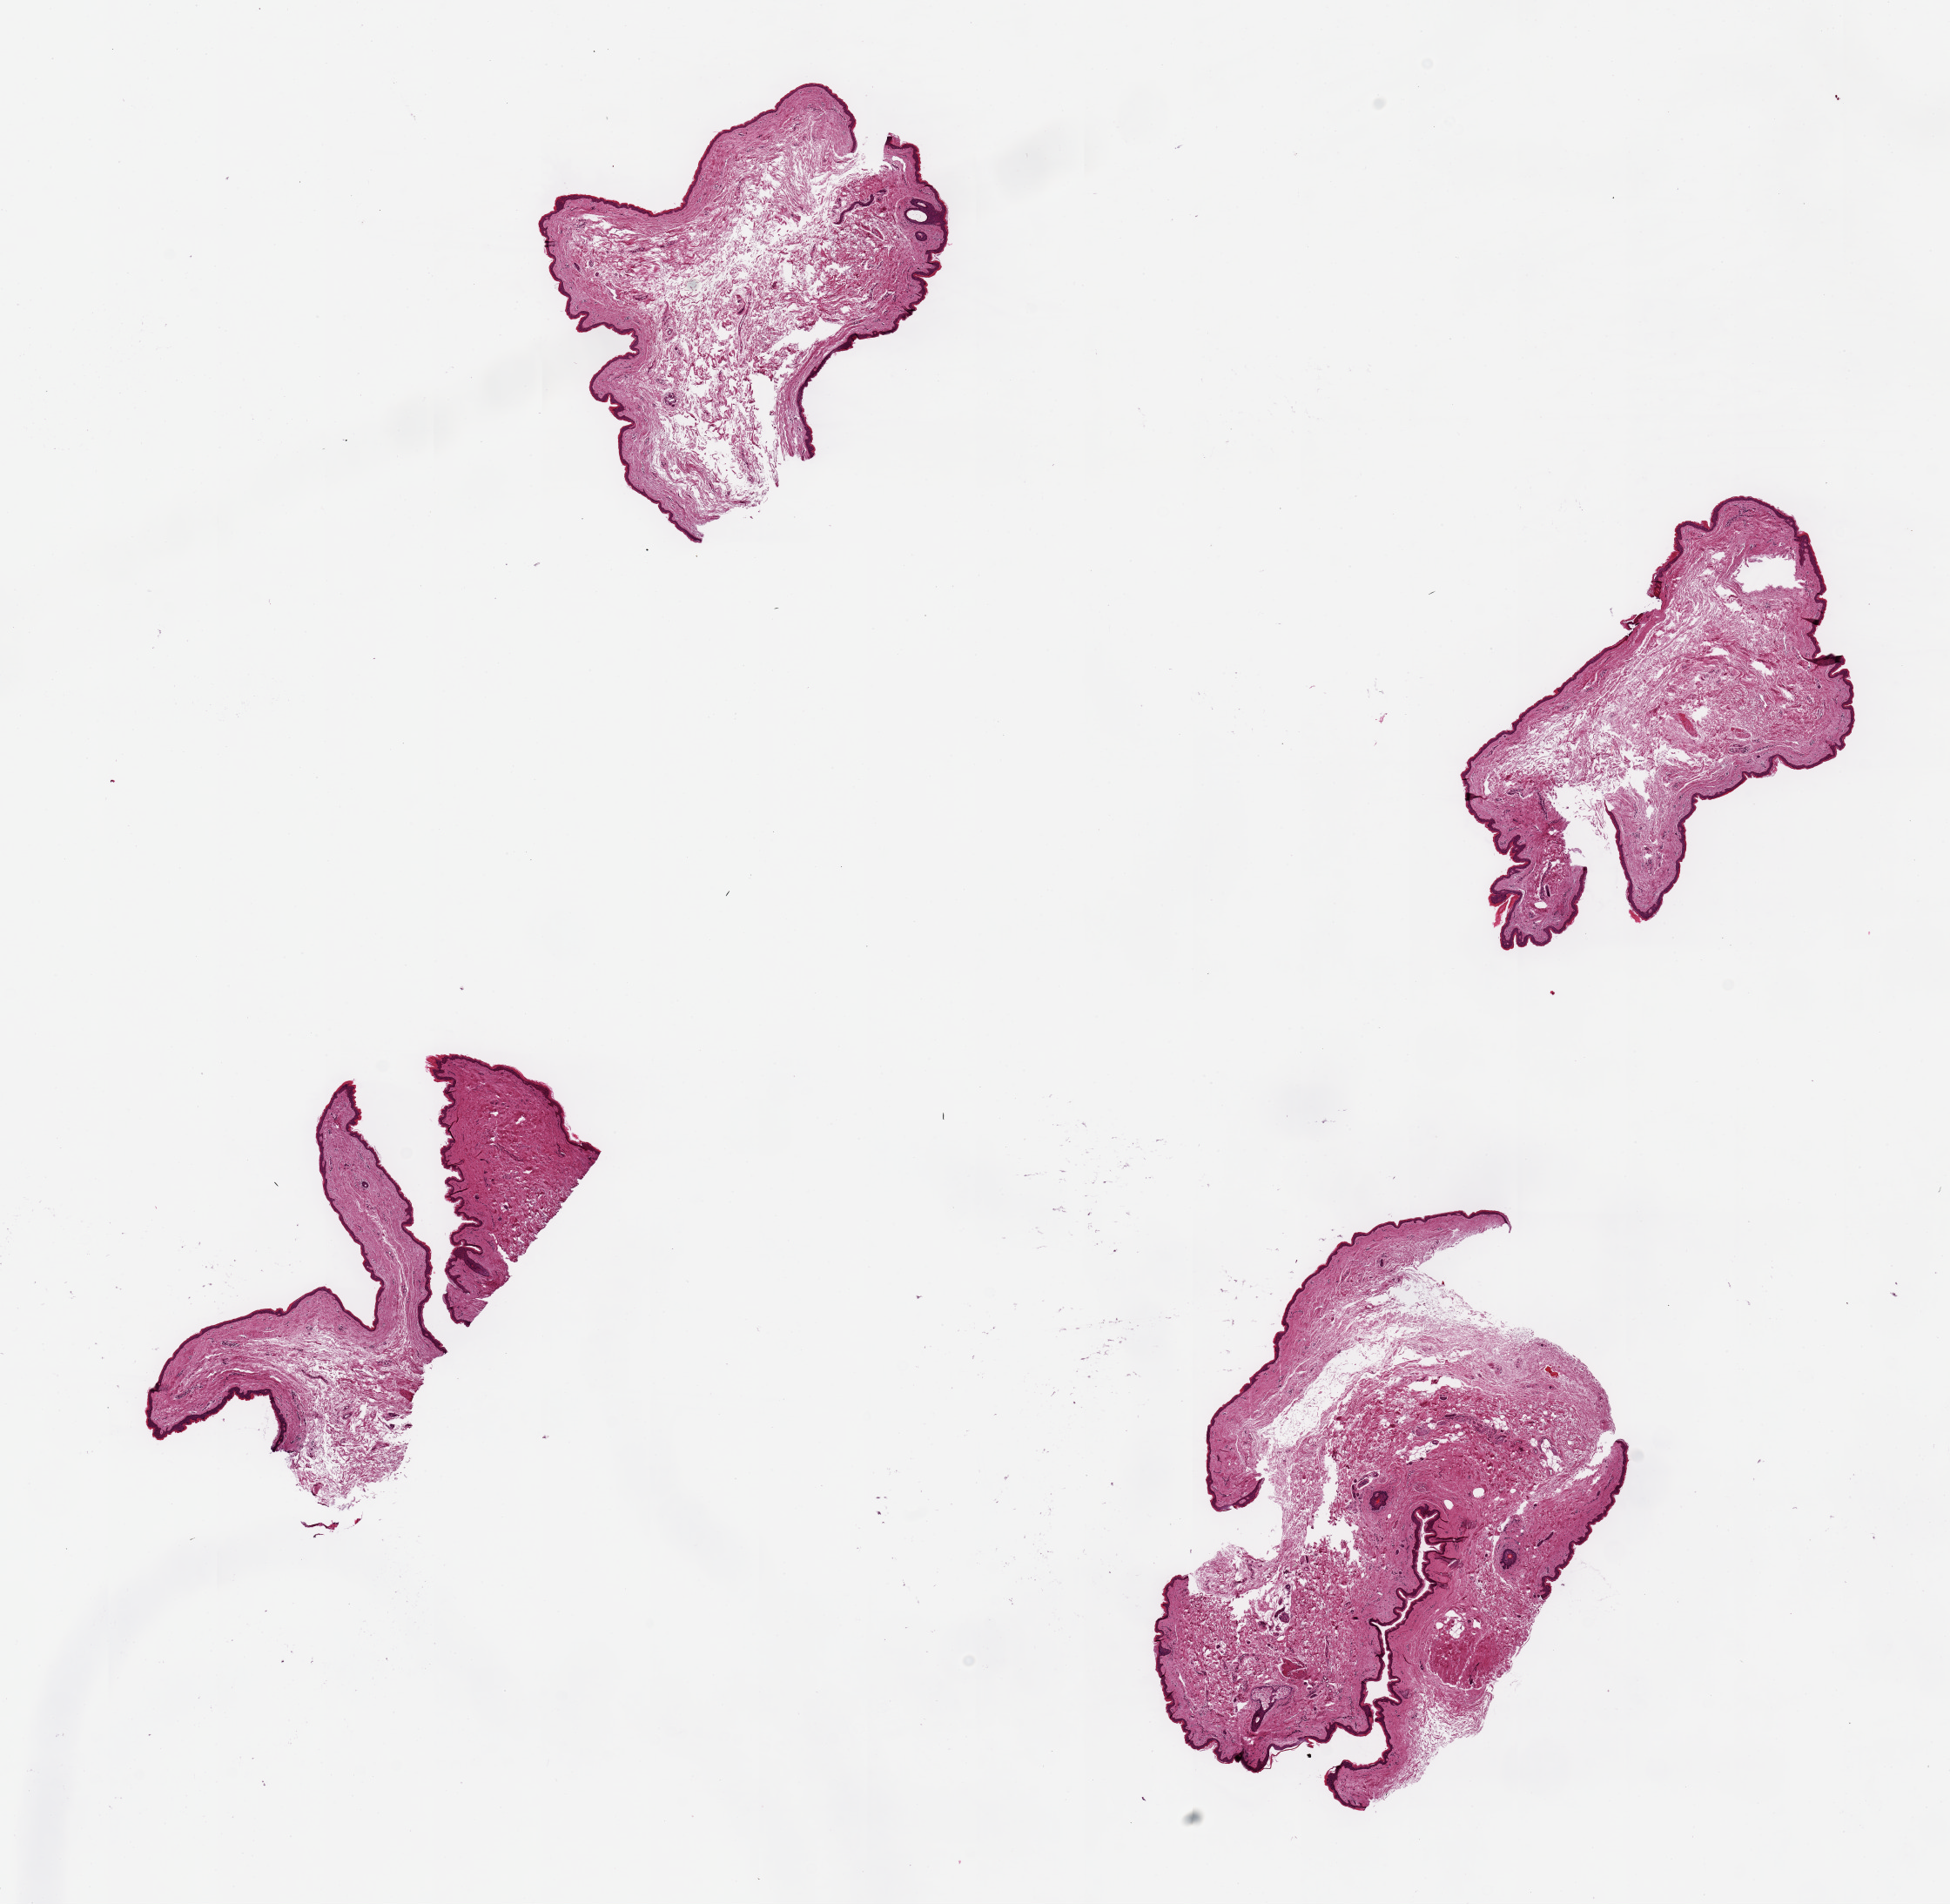
Whole-slide image, haematoxylin and eosin stain, whole scanned area (about 17.7 x 17.3 mm) shown as a low-resolution overview. PAXgene-fixed paraffin-embedded (PFPE) section. Target tissue: skin of suprapubic region. Tissue donor sample. Donor: female.
Reviewer comment on this tissue sample: 4 pieces, up to 6x3mm;squamous epitheliums is ~2-3% thickness.